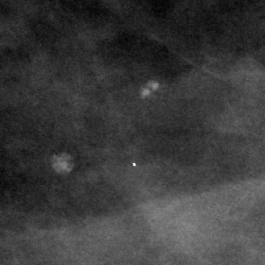
Cropped region of a digitized screen-film mammogram centred on a radiologist-marked abnormality; right breast; CC view; BI-RADS breast density category 2 (scale 1–4).
Marked abnormality: calcifications, morphology pleomorphic, distribution clustered; BI-RADS assessment category 2; benign; no additional work-up was recommended (benign without callback).